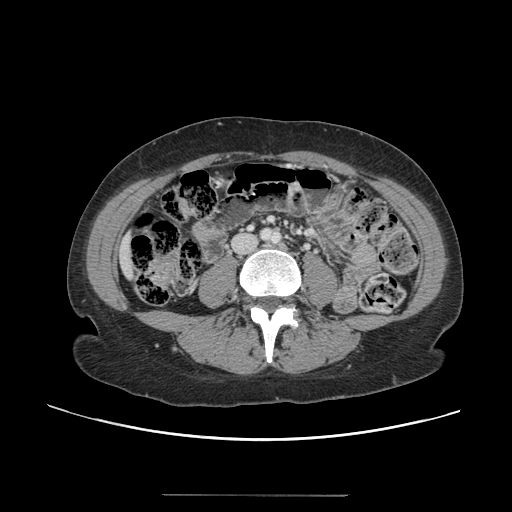
Contrast-enhanced abdominal CT, one axial slice. Slice 14 of 144 in the series (ordered by position). 120 kVp. Intravenous contrast given. Soft-tissue window (W 400 / L 40 HU). 2.5 mm slice thickness. 512 × 512 image matrix, field of view 380 × 380 mm. Female patient, age 53 years. Case-level facts recorded for this patient, not image findings: diagnosis: colorectal cancer liver metastases, imaged before liver resection; multiple liver metastases: yes; largest metastasis: 1.1 cm; disease in both lobes: no.
Annotated regions visible in this slice (manually delineated by an expert):
- liver: bounding box [x1, y1, x2, y2] px = [120, 237, 134, 278]
- planned liver remnant (the part of the liver to remain after resection): [117, 238, 134, 279]